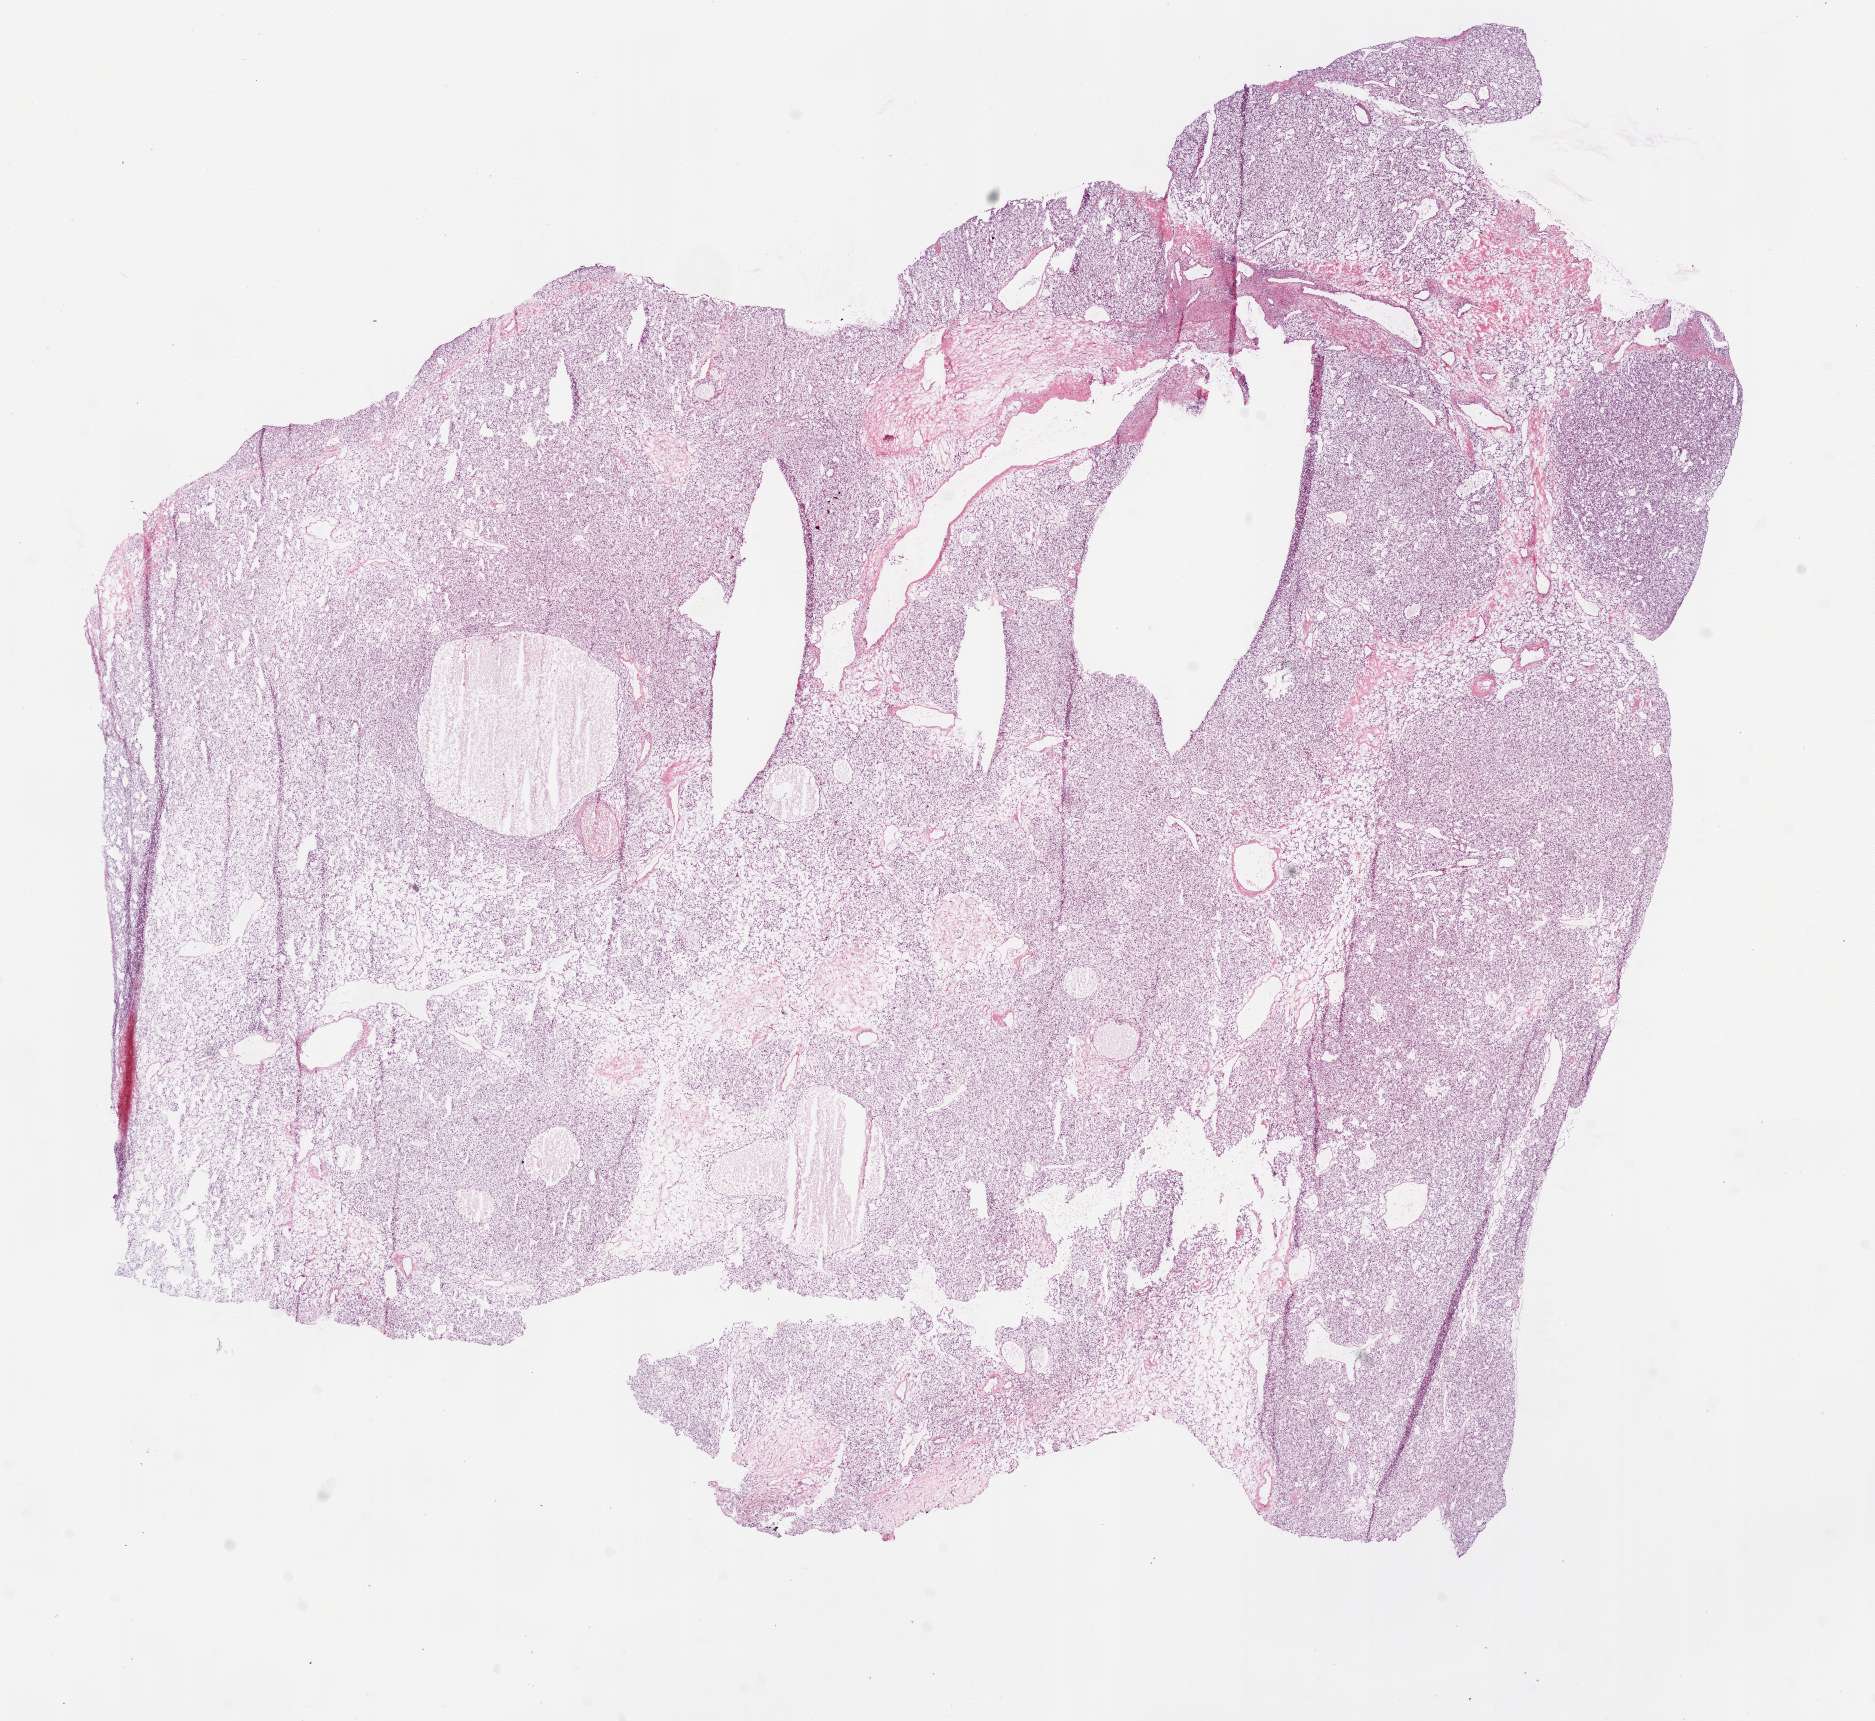
Whole-slide histology image, H&E — a low-resolution overview of the entire scanned area, about 15.0 x 13.8 mm. Frozen section from the bottom of the tissue portion. Sample: primary tumour, kidney. Patient: male, age at initial diagnosis 47 years. Histologic grade: G2 (moderately differentiated). Pathologist review of this section (percent, as recorded): tumour cells 85%, tumour nuclei 85%, normal cells 0%, stromal cells 15%, necrosis 0%.
Pathologic diagnosis: Clear cell adenocarcinoma, NOS. TNM: T1a NX M0. AJCC pathologic stage: I.